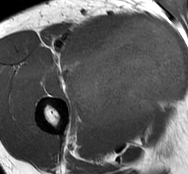
MRI of an extremity soft-tissue mass, one axial slice; slice 49 of 93 in the series (ordered by position); MR volume resampled by the dataset authors to the PET/CT grid (not the native acquisition matrix); 188 × 174 image matrix, field of view 184 × 170 mm. Male patient. From the clinical record (not read from this slice): histological type: undifferentiated - pleiomorphic; grade: high; site of the primary tumour: right thigh.
Annotated regions visible in this slice (expert contour drawn on MRI and transferred to this co-registered scan by the dataset authors):
- gross tumour volume including surrounding oedema: bounding box (x1, y1, x2, y2) in pixels: (68, 17, 185, 130)
- gross tumour volume (mass): (74, 19, 185, 129)